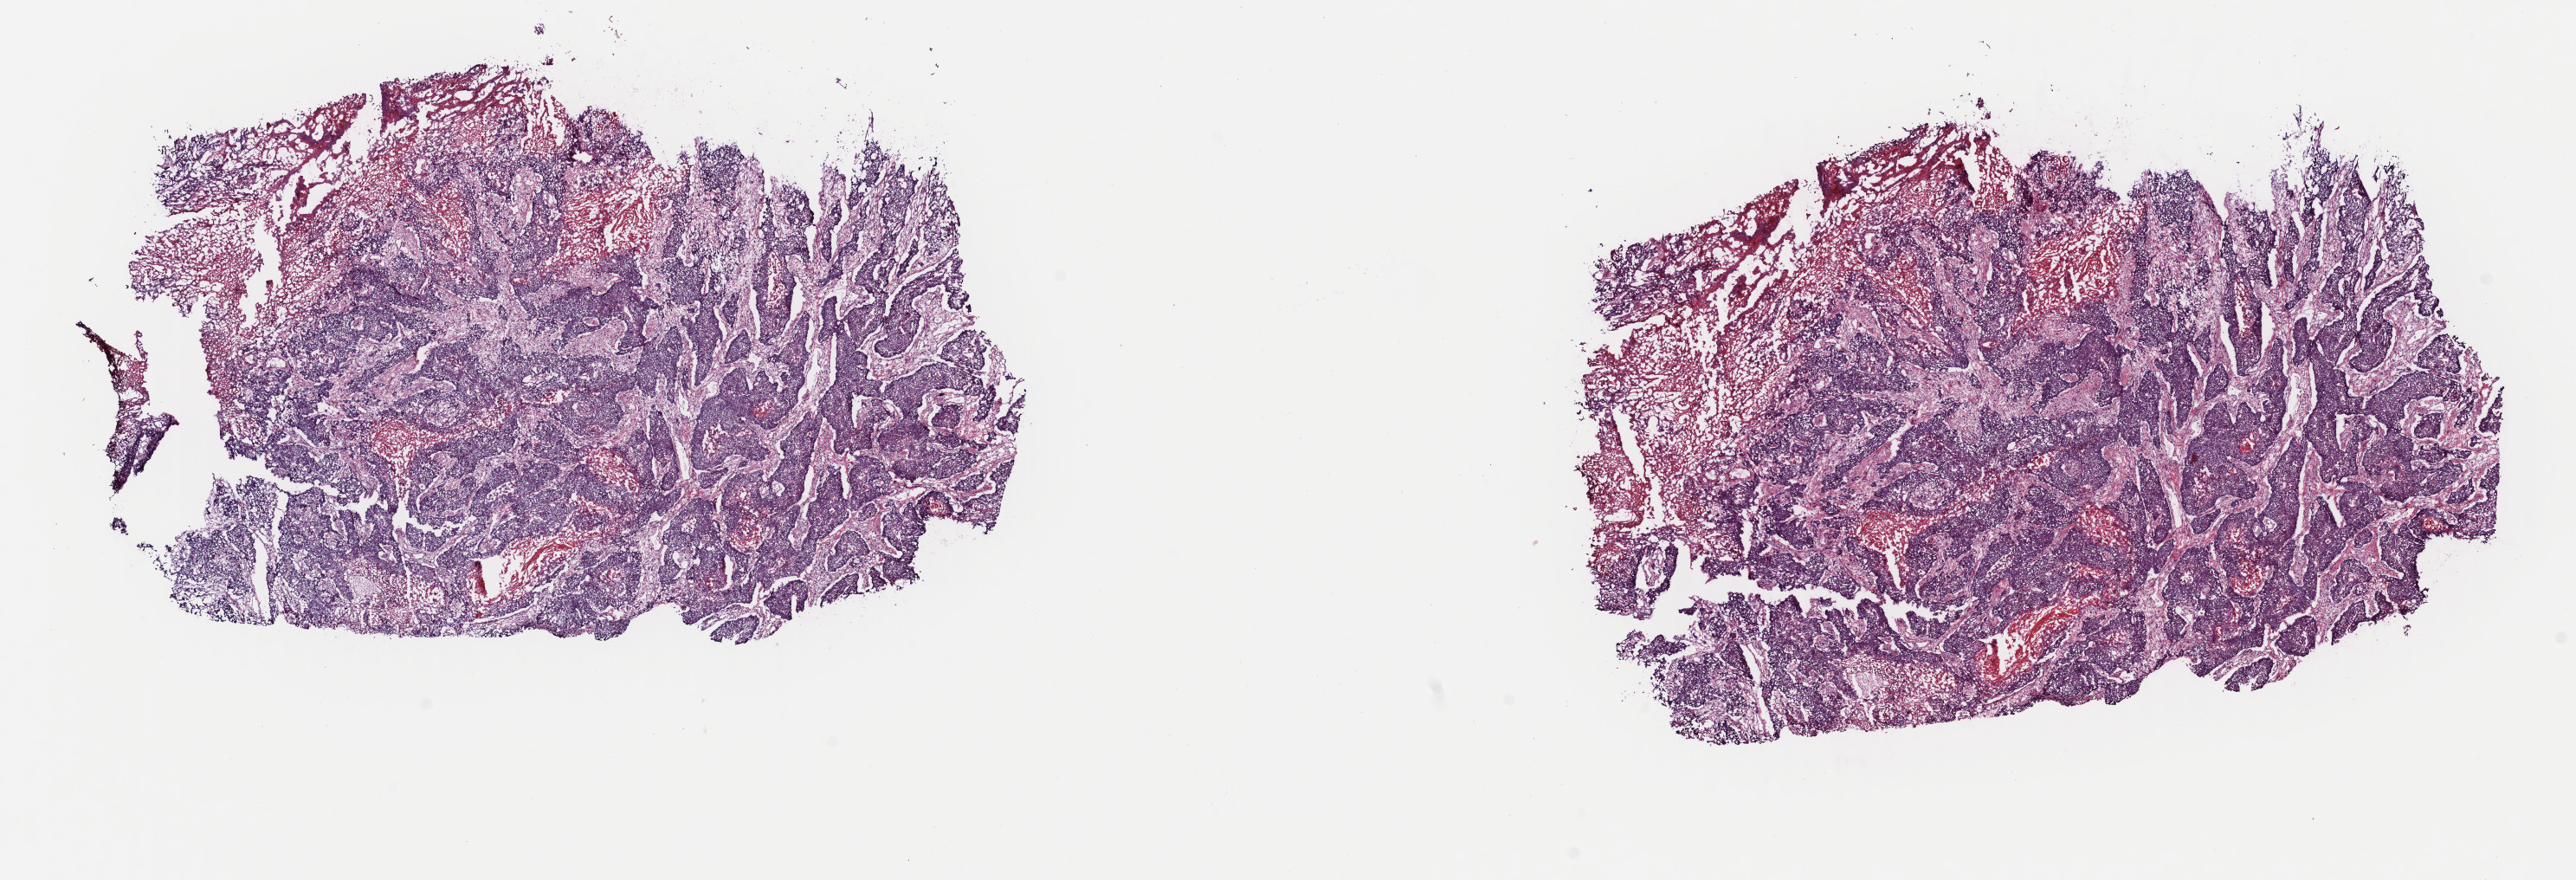
Hematoxylin and eosin (H&E) stained whole-slide image — shown as a low-resolution overview of the whole scanned area (about 23.5 x 8.0 mm, slide scanned at 40x); frozen section from the top of the tissue portion; sample: primary tumour, head and neck. Male, age 66 years at initial diagnosis. Histologic grade: G2 (moderately differentiated). Composition of this section per pathologist review: tumour cells 70%, tumour nuclei 80%, normal cells 0%, stromal cells 20%, necrosis 10%. Inflammatory infiltration, as recorded: lymphocyte infiltration 5%, monocyte infiltration 0%, neutrophil infiltration 0%.
Lymph nodes positive (case pathology): 0 of 40 examined. Diagnosis: Squamous cell carcinoma, NOS (floor of mouth, NOS). AJCC pathologic stage: IVA.